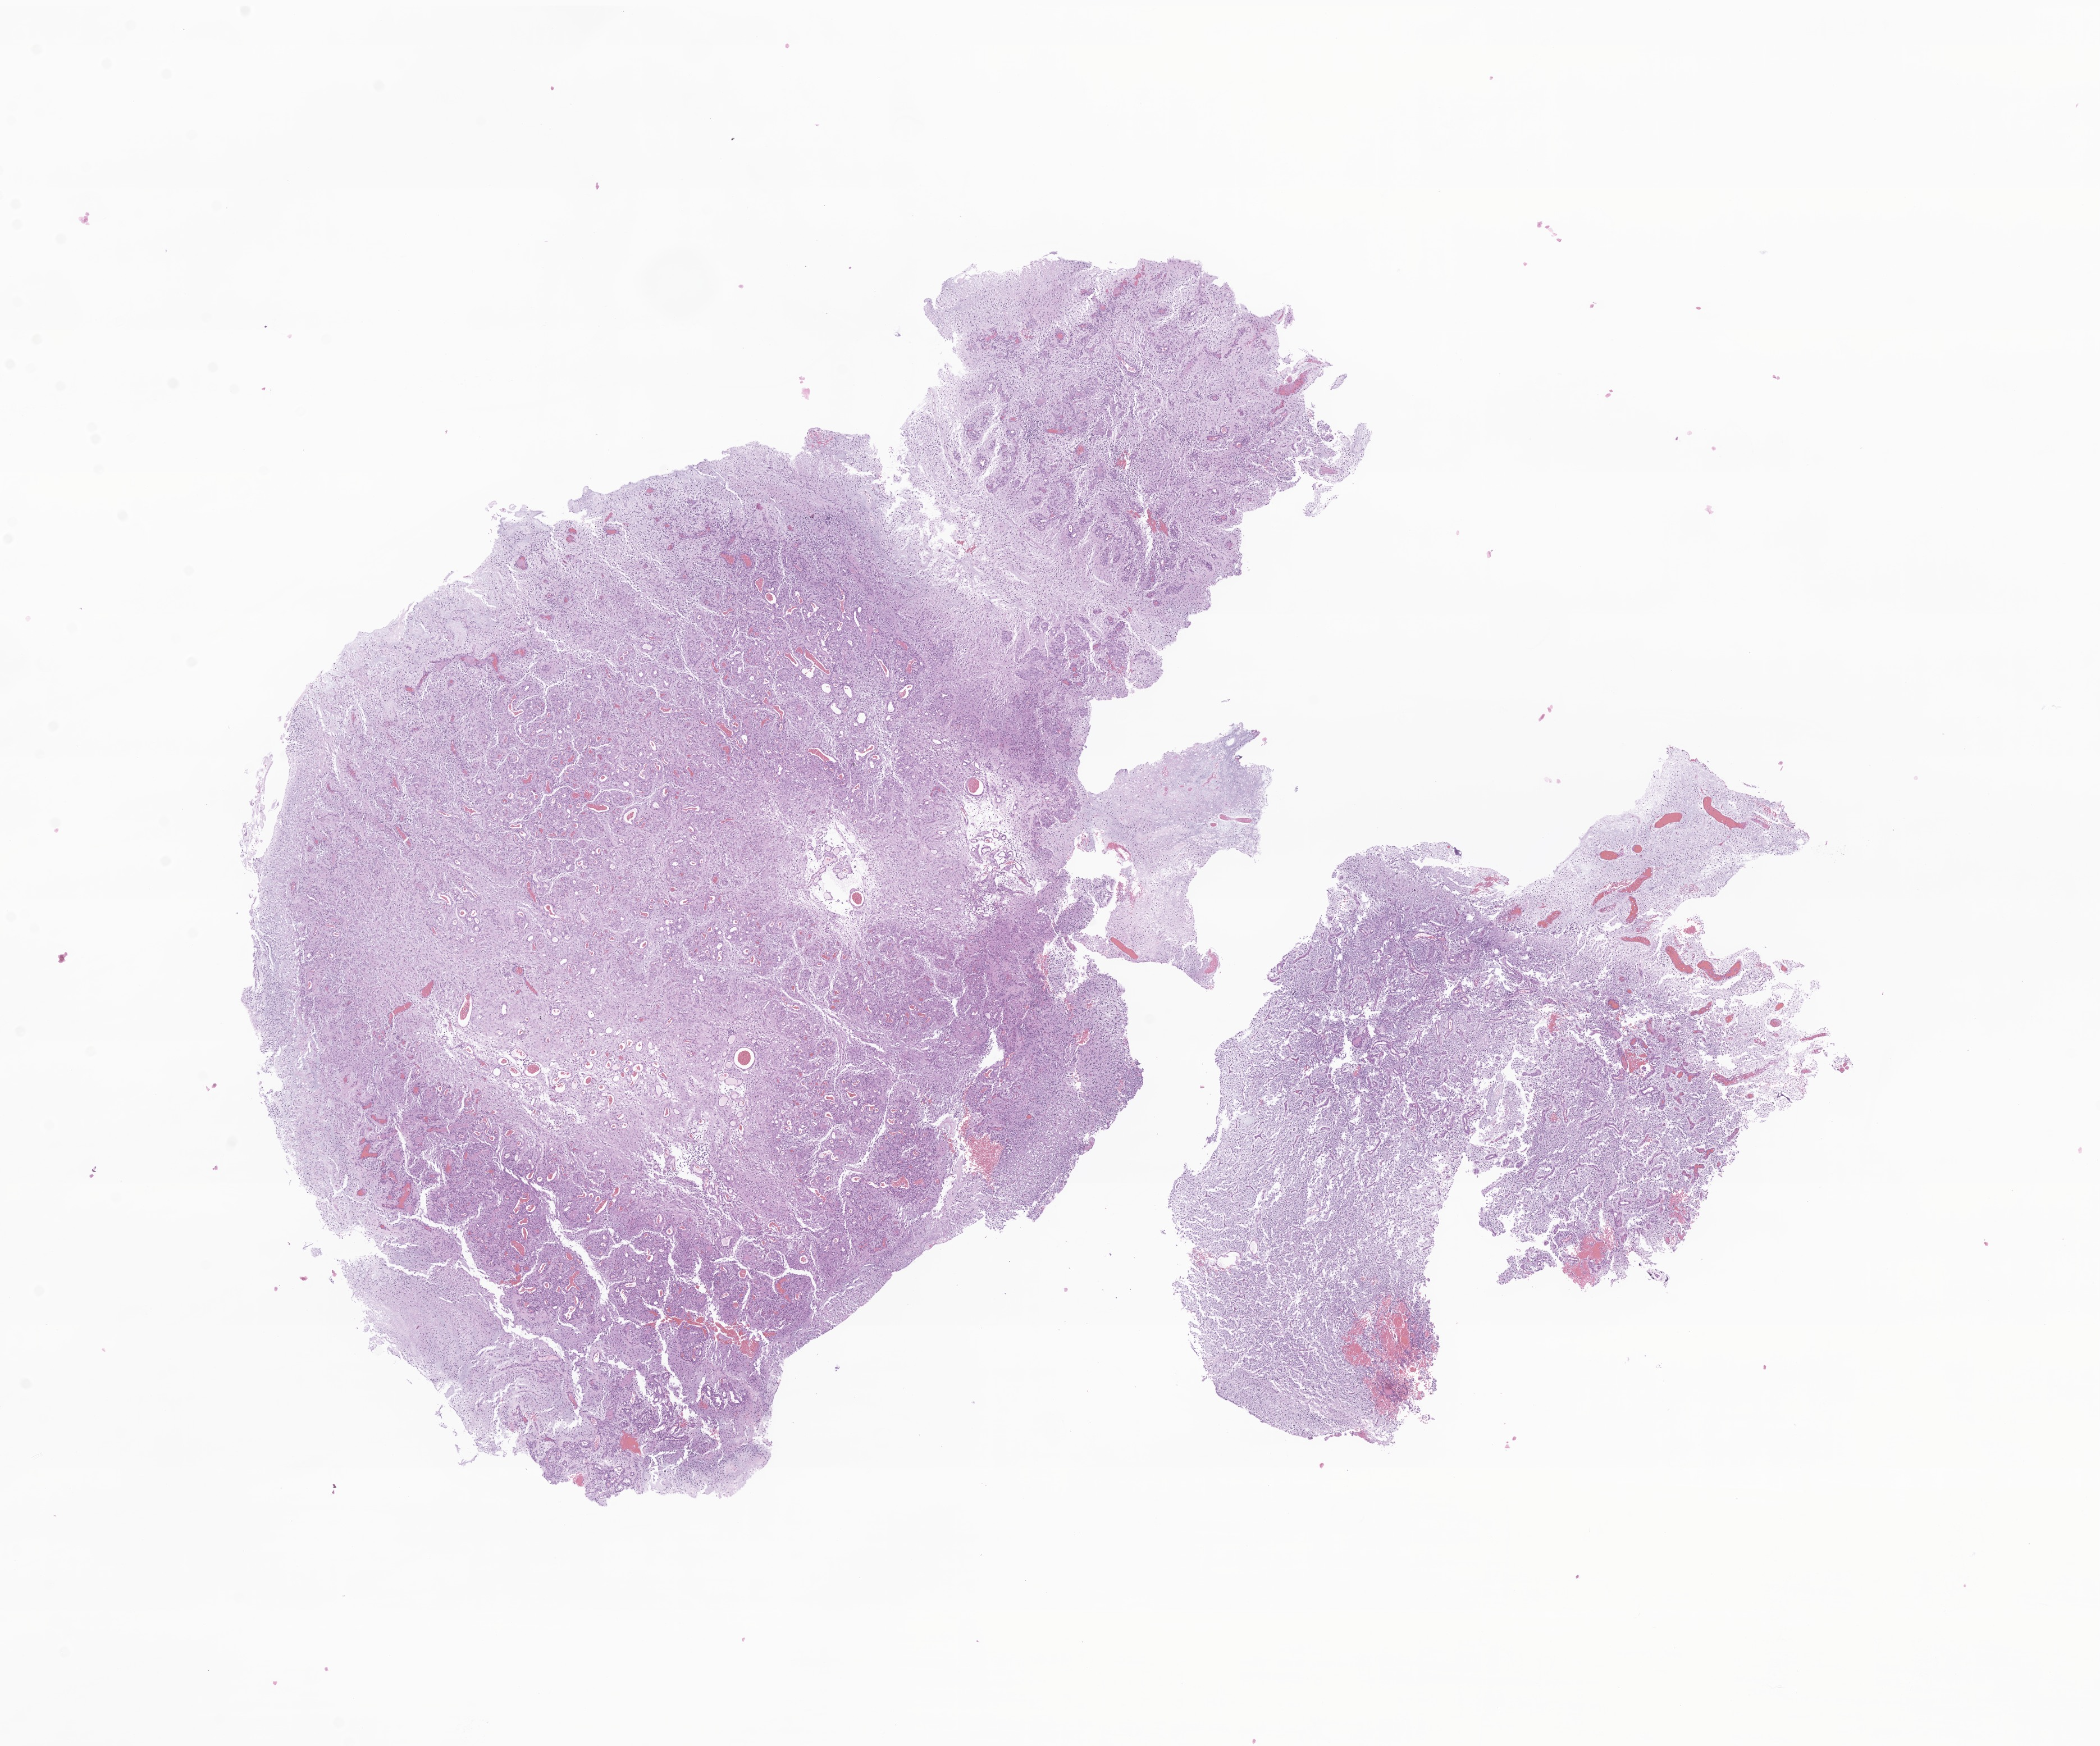
H&E whole-slide image of tumor tissue from the brain — whole scanned area (about 15.8 x 13.1 mm) shown as a low-resolution overview. FFPE section. Patient: female, age 95 months.
Diagnosis: Astrocytoma, NOS.